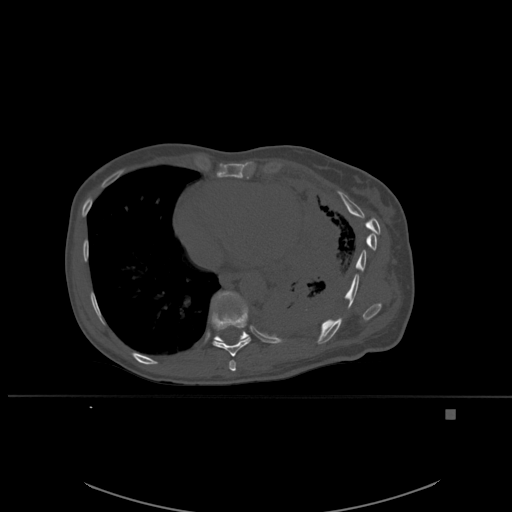
CT including the spine, one axial slice; position 330 of 537 along the scan axis; bone window (W 1800 / L 400 HU); 1.5 mm slice thickness; 512 × 512 image matrix. Female patient, age 45 years. Case-level facts recorded for this patient, not image findings: primary cancer: lung.
Outlined on this slice (semi-automatically segmented with operator editing):
- T10 vertebra: box from (x=212, y=291) to (x=249, y=344) px
- T8 vertebra: (x=229, y=360)–(x=236, y=372)
- T9 vertebra: (x=210, y=294)–(x=251, y=357)